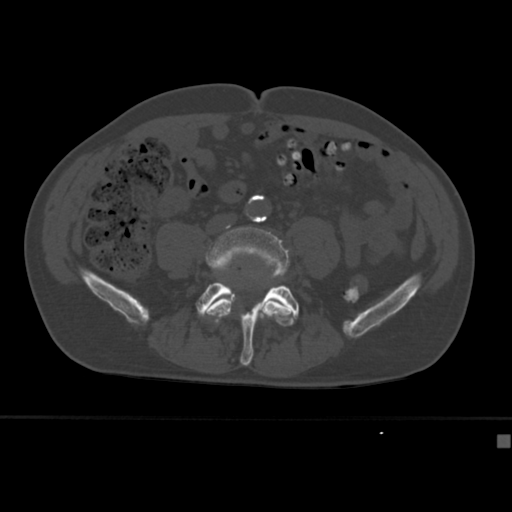
CT including the spine, one axial slice; position 96 of 430 along the scan axis; reconstruction kernel Br40s; 120 kVp; bone window (W 1800 / L 400 HU); 1.5 mm slice thickness; 512 × 512 image matrix. Male patient, age 64 years. Case-level facts recorded for this patient, not image findings: primary cancer: uterus.
Structures marked on this image (semi-automatic segmentation, software-assisted and operator-edited):
- L4 vertebra: bounding box [x1, y1, x2, y2] px = [205, 224, 293, 325]
- L5 vertebra: [196, 282, 299, 366]